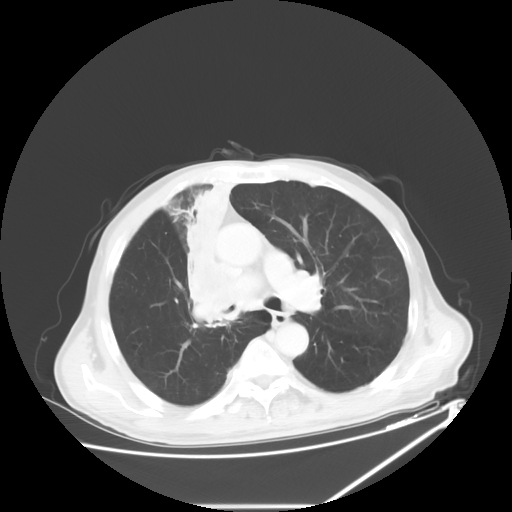
Chest CT, one axial slice. Slice 39 of 60 in the series (ordered by position). Reconstruction kernel STANDARD. 120 kVp. Lung window (W 1500 / L -600 HU). 5 mm slice thickness. 512 × 512 image matrix, field of view 410 × 410 mm. Patient: male, 73 years. Case-level facts recorded for this patient, not image findings: clinical TNM (as recorded): T2a N1 M0.
Outlined on this slice (bounding box drawn by a radiologist):
- lung tumour (recorded histology: squamous cell carcinoma): bounding box [x1, y1, x2, y2] px = [161, 177, 253, 340]